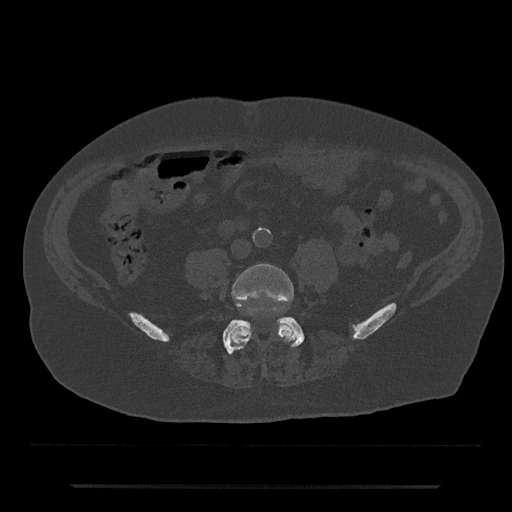
CT including the spine, one axial slice. Position 321 of 797 along the scan axis. Bone window (W 1800 / L 400 HU). 0.5 mm slice thickness. 512 × 512 image matrix, field of view 434 × 434 mm. Male patient, age 80 years. From the clinical record (not read from this slice): primary cancer: prostate.
Outlined on this slice (semi-automatic segmentation, software-assisted and operator-edited):
- L4 vertebra: bounding box <228,263,297,349> (left, top, right, bottom; pixels)
- L5 vertebra: <223,317,305,354>